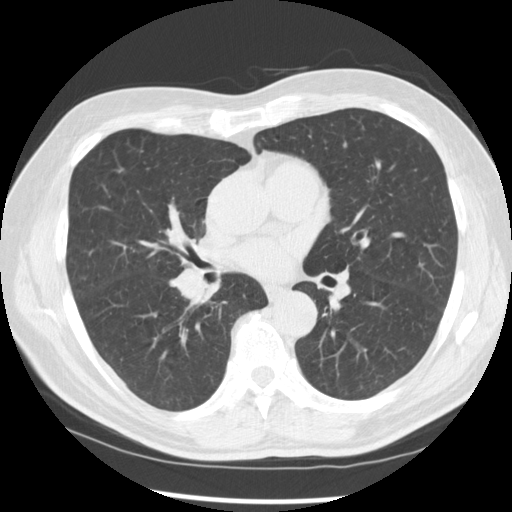
Low-dose screening chest CT, axial slice, baseline annual screen, lung window (W 1500 / L -600 HU), 2.5 mm slice thickness, slice 146 of 277 in the series, 512 × 512 image matrix. Male participant, aged 67 years at enrolment. Current smoker at enrolment.
Expert-annotated lung lesion, bounding box (x1, y1, x2, y2) in pixels: (157, 246, 228, 312). Screening reader's record for this exam (one nodule recorded; not confirmed to be the boxed lesion): non-calcified nodule or mass ≥4 mm, left lower lobe, 15 × 15 mm, spiculated (stellate) margins, soft tissue attenuation. Note: the box lies in the patient's right hemithorax on this image, whereas the reader's record names the left lung; they may be different findings.